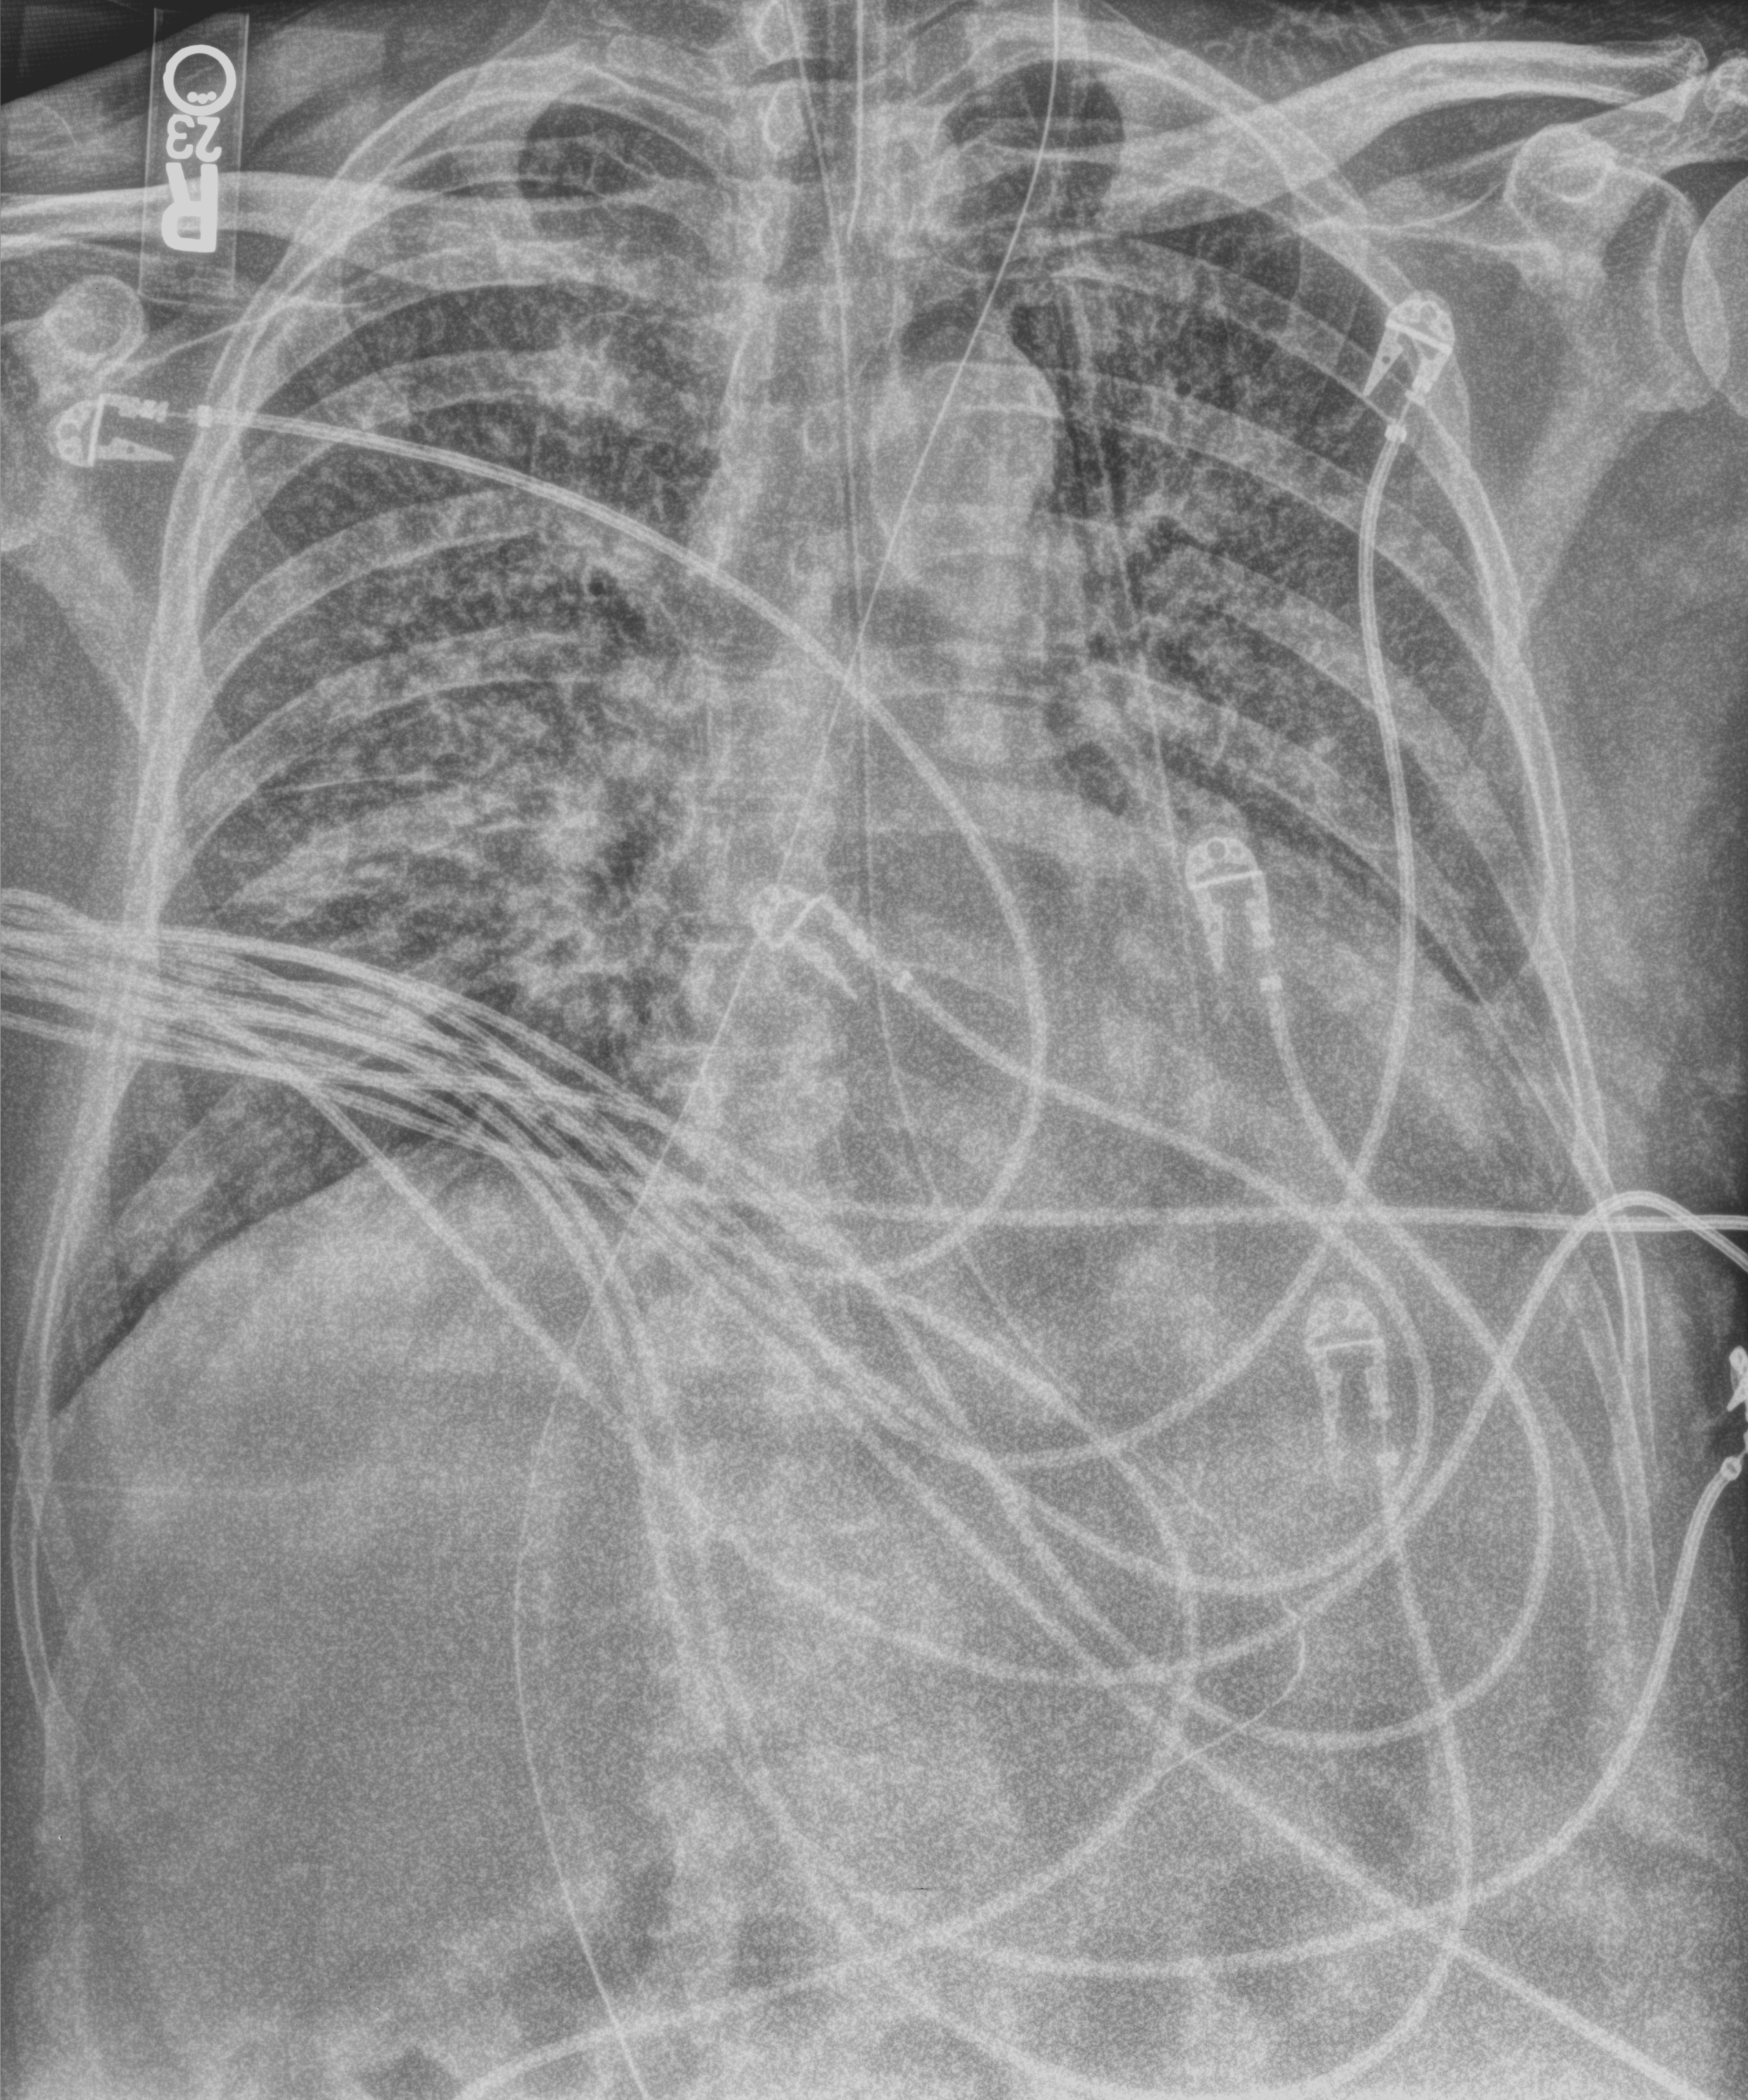
Bedside chest radiograph (computed radiography); anteroposterior (AP) projection. Patient hospitalised with COVID-19; male, aged 60–74 years.
From the hospital-stay record, not from the radiograph (when in the stay this image was taken is not recorded): admitted to intensive care during this hospital stay: yes; diabetes (admission record): no; mechanically ventilated during this hospital stay: yes.